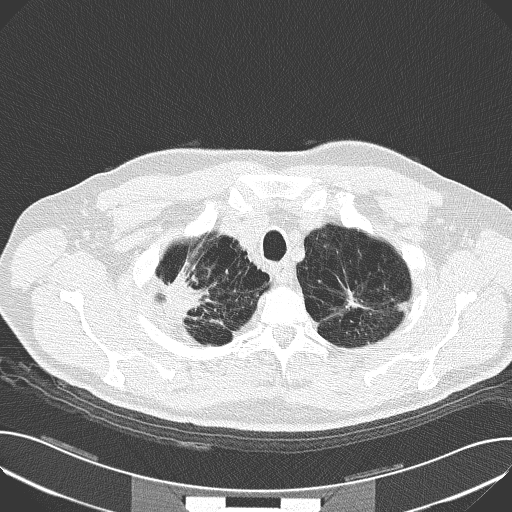
Axial slice from a low-dose chest CT screening exam. First (baseline) screen. Lung window (W 1500 / L -600 HU). Slice 18 of 159 in the series. Male, age 59 years at enrolment. Current smoker at enrolment.
Lesion marked by an expert reader, box from (x=155, y=260) to (x=222, y=332) px. The screening reader recorded 4 non-calcified nodules or masses ≥4 mm on this exam; which of them this box marks is not recorded. Lung cancer was diagnosed 44 days after this screen: squamous cell carcinoma, NOS, right upper lobe, moderately differentiated (G2), stage IA (AJCC 6th edition), 30 mm at pathology.